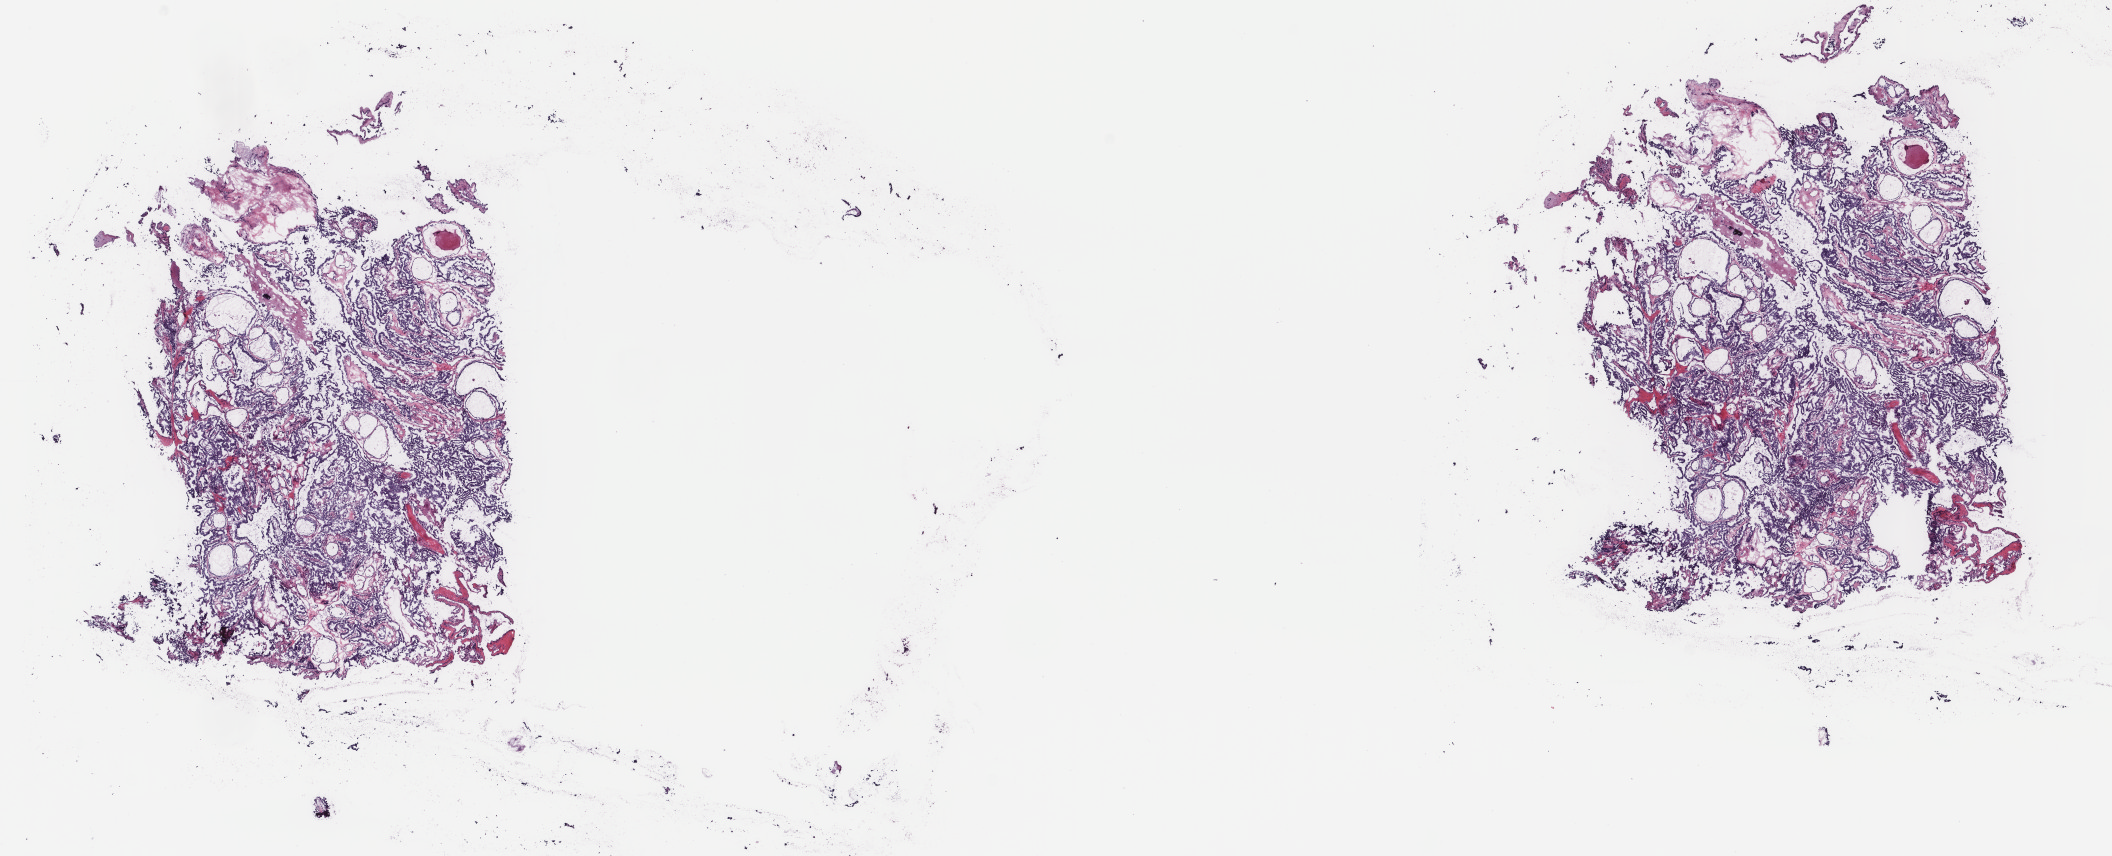
Digitized Hematoxylin and eosin (H&E) stained tissue section (whole slide) — low-resolution overview of the scanned area, about 16.8 x 6.8 mm, frozen section from the top of the tissue portion, thyroid, primary tumour sample. Patient: female, age at initial diagnosis 28 years. Slide review estimates, as recorded: tumour cells 70%, tumour nuclei 100%, normal cells 0%, stromal cells 30%, necrosis 0%. Inflammatory infiltration, as recorded: lymphocyte infiltration 0%, monocyte infiltration 1%, neutrophil infiltration 0%.
AJCC pathologic stage: I. Diagnosis: Papillary adenocarcinoma, NOS (thyroid gland).